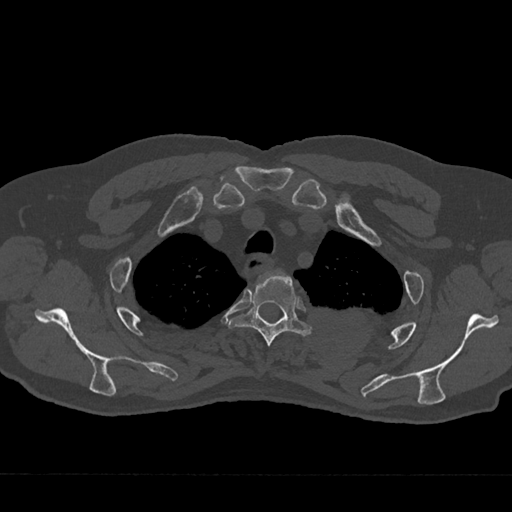
CT including the spine, one axial slice. Slice 573 of 797 in the series (ordered by position). Bone window (W 1800 / L 400 HU). 0.5 mm slice thickness. 512 × 512 image matrix, field of view 377 × 377 mm. Patient: male, 75 years. From the clinical record (not read from this slice): primary cancer: renal; vertebrae with lytic lesions (as recorded): T4.
Structures marked on this image (semi-automatically segmented with operator editing):
- T3 vertebra: bounding box [x1, y1, x2, y2] px = [230, 272, 312, 346]